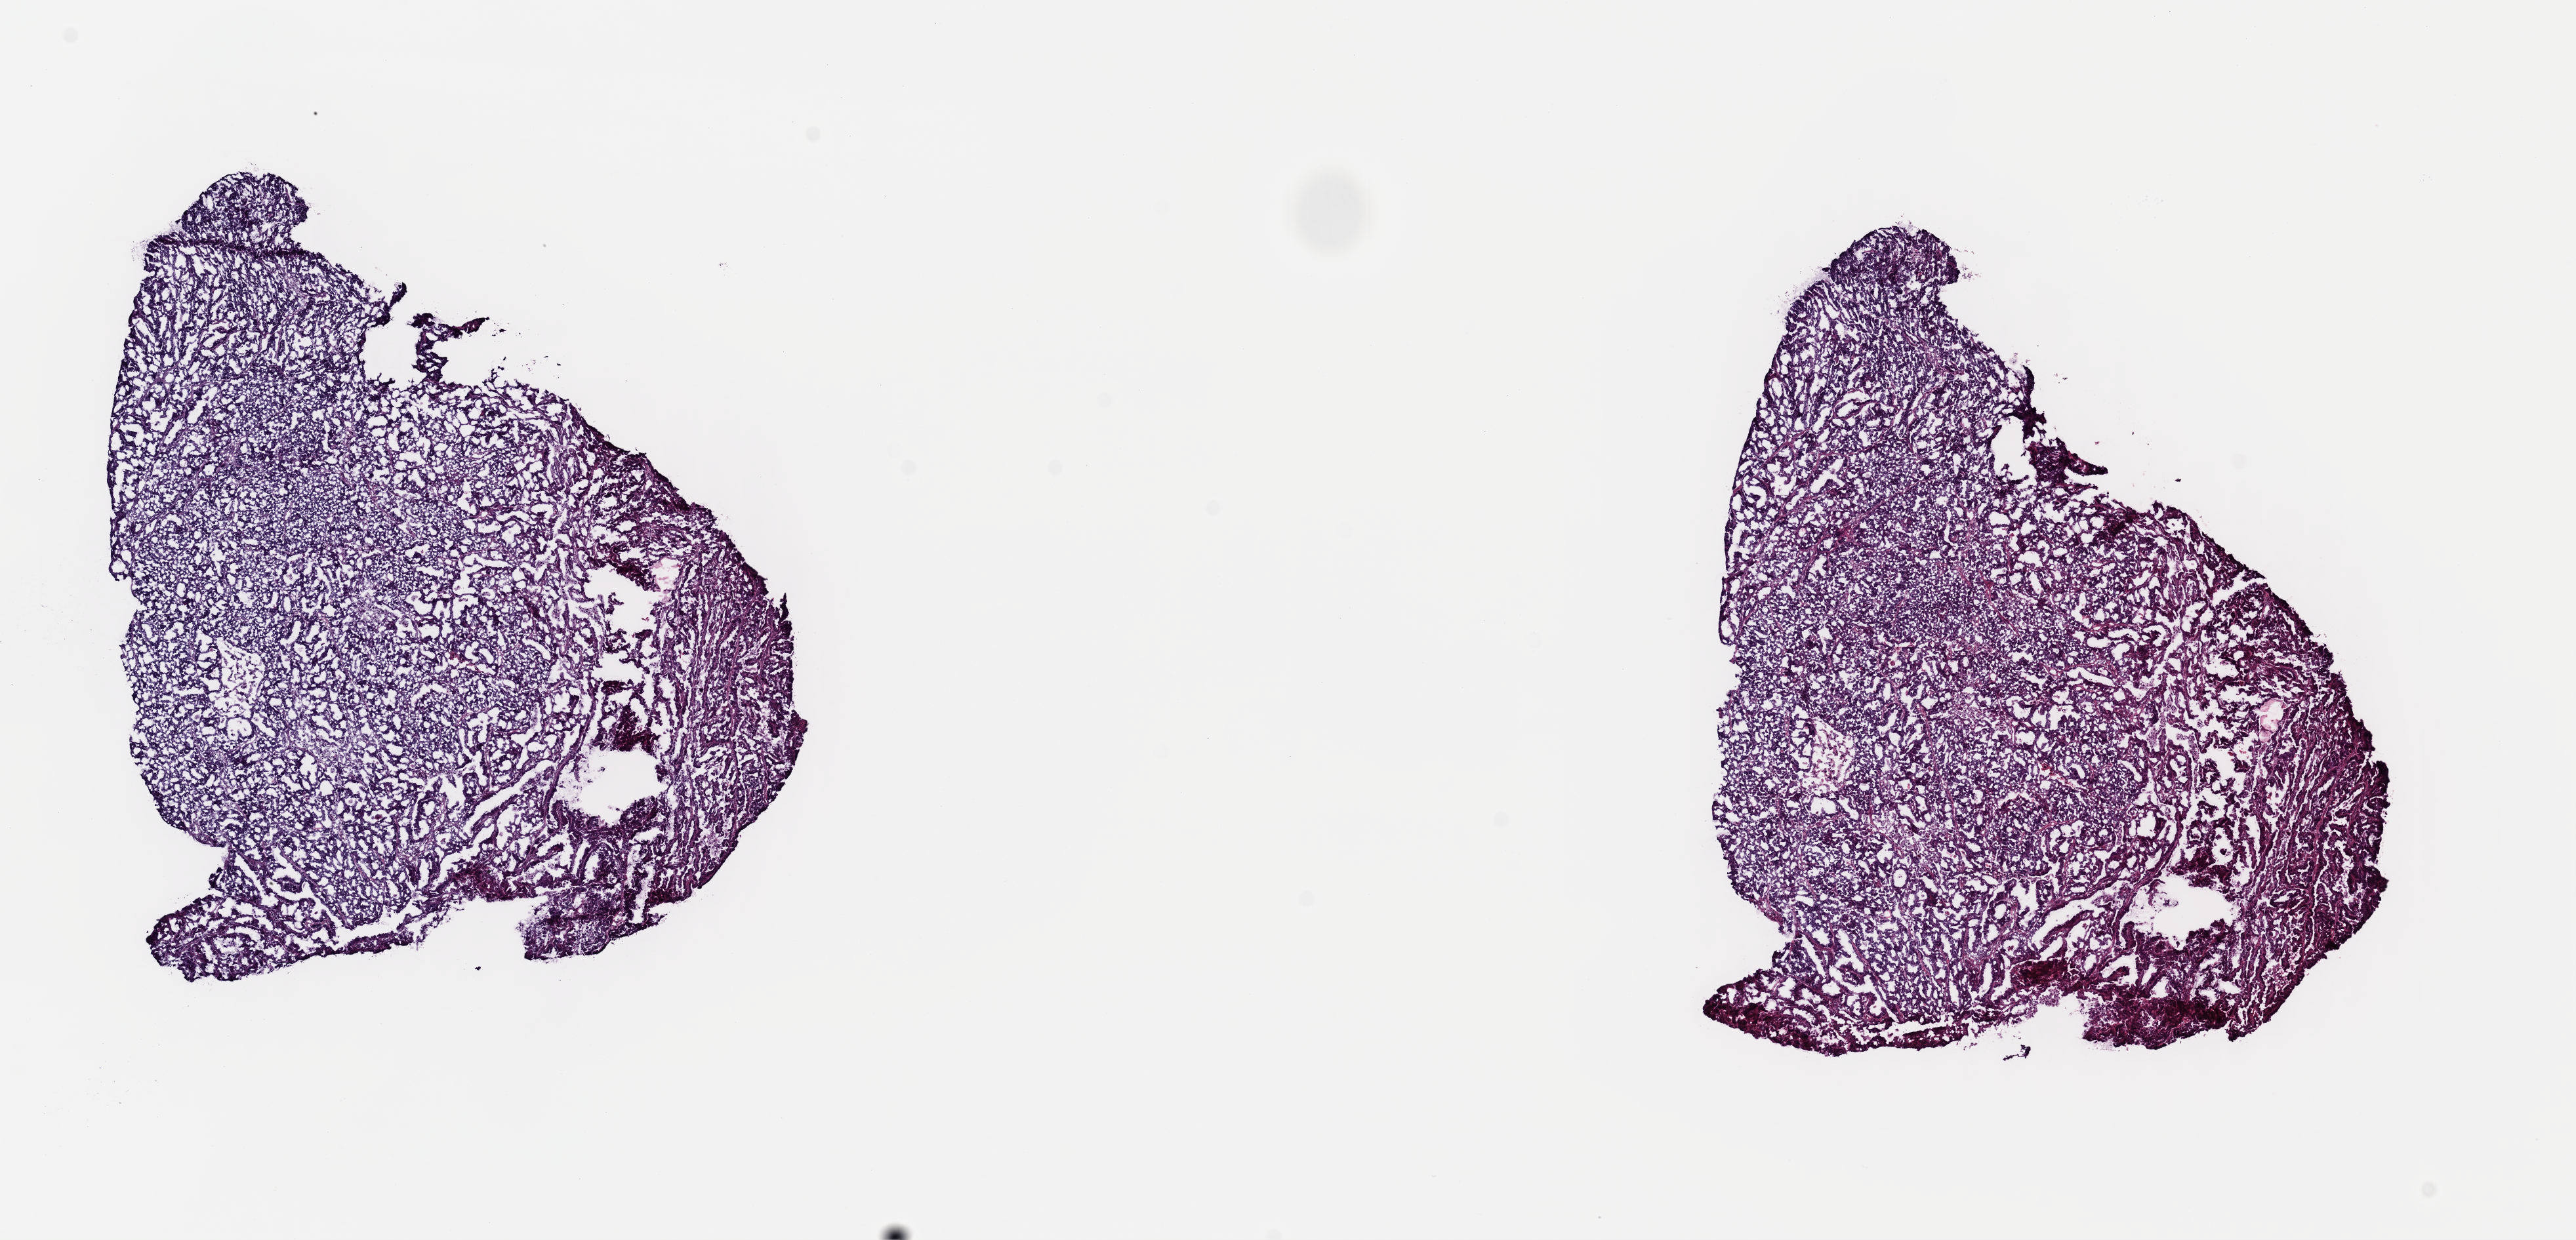
Digitized H&E tissue section (whole slide) — a low-resolution overview of the entire scanned area, about 15.5 x 7.5 mm (acquisition: 40x scan); frozen section from the top of the tissue portion; primary tumour sample from the uterus. Female patient; age at initial diagnosis 77 years.
Pathologic diagnosis: Endometrioid adenocarcinoma, NOS (endometrium).